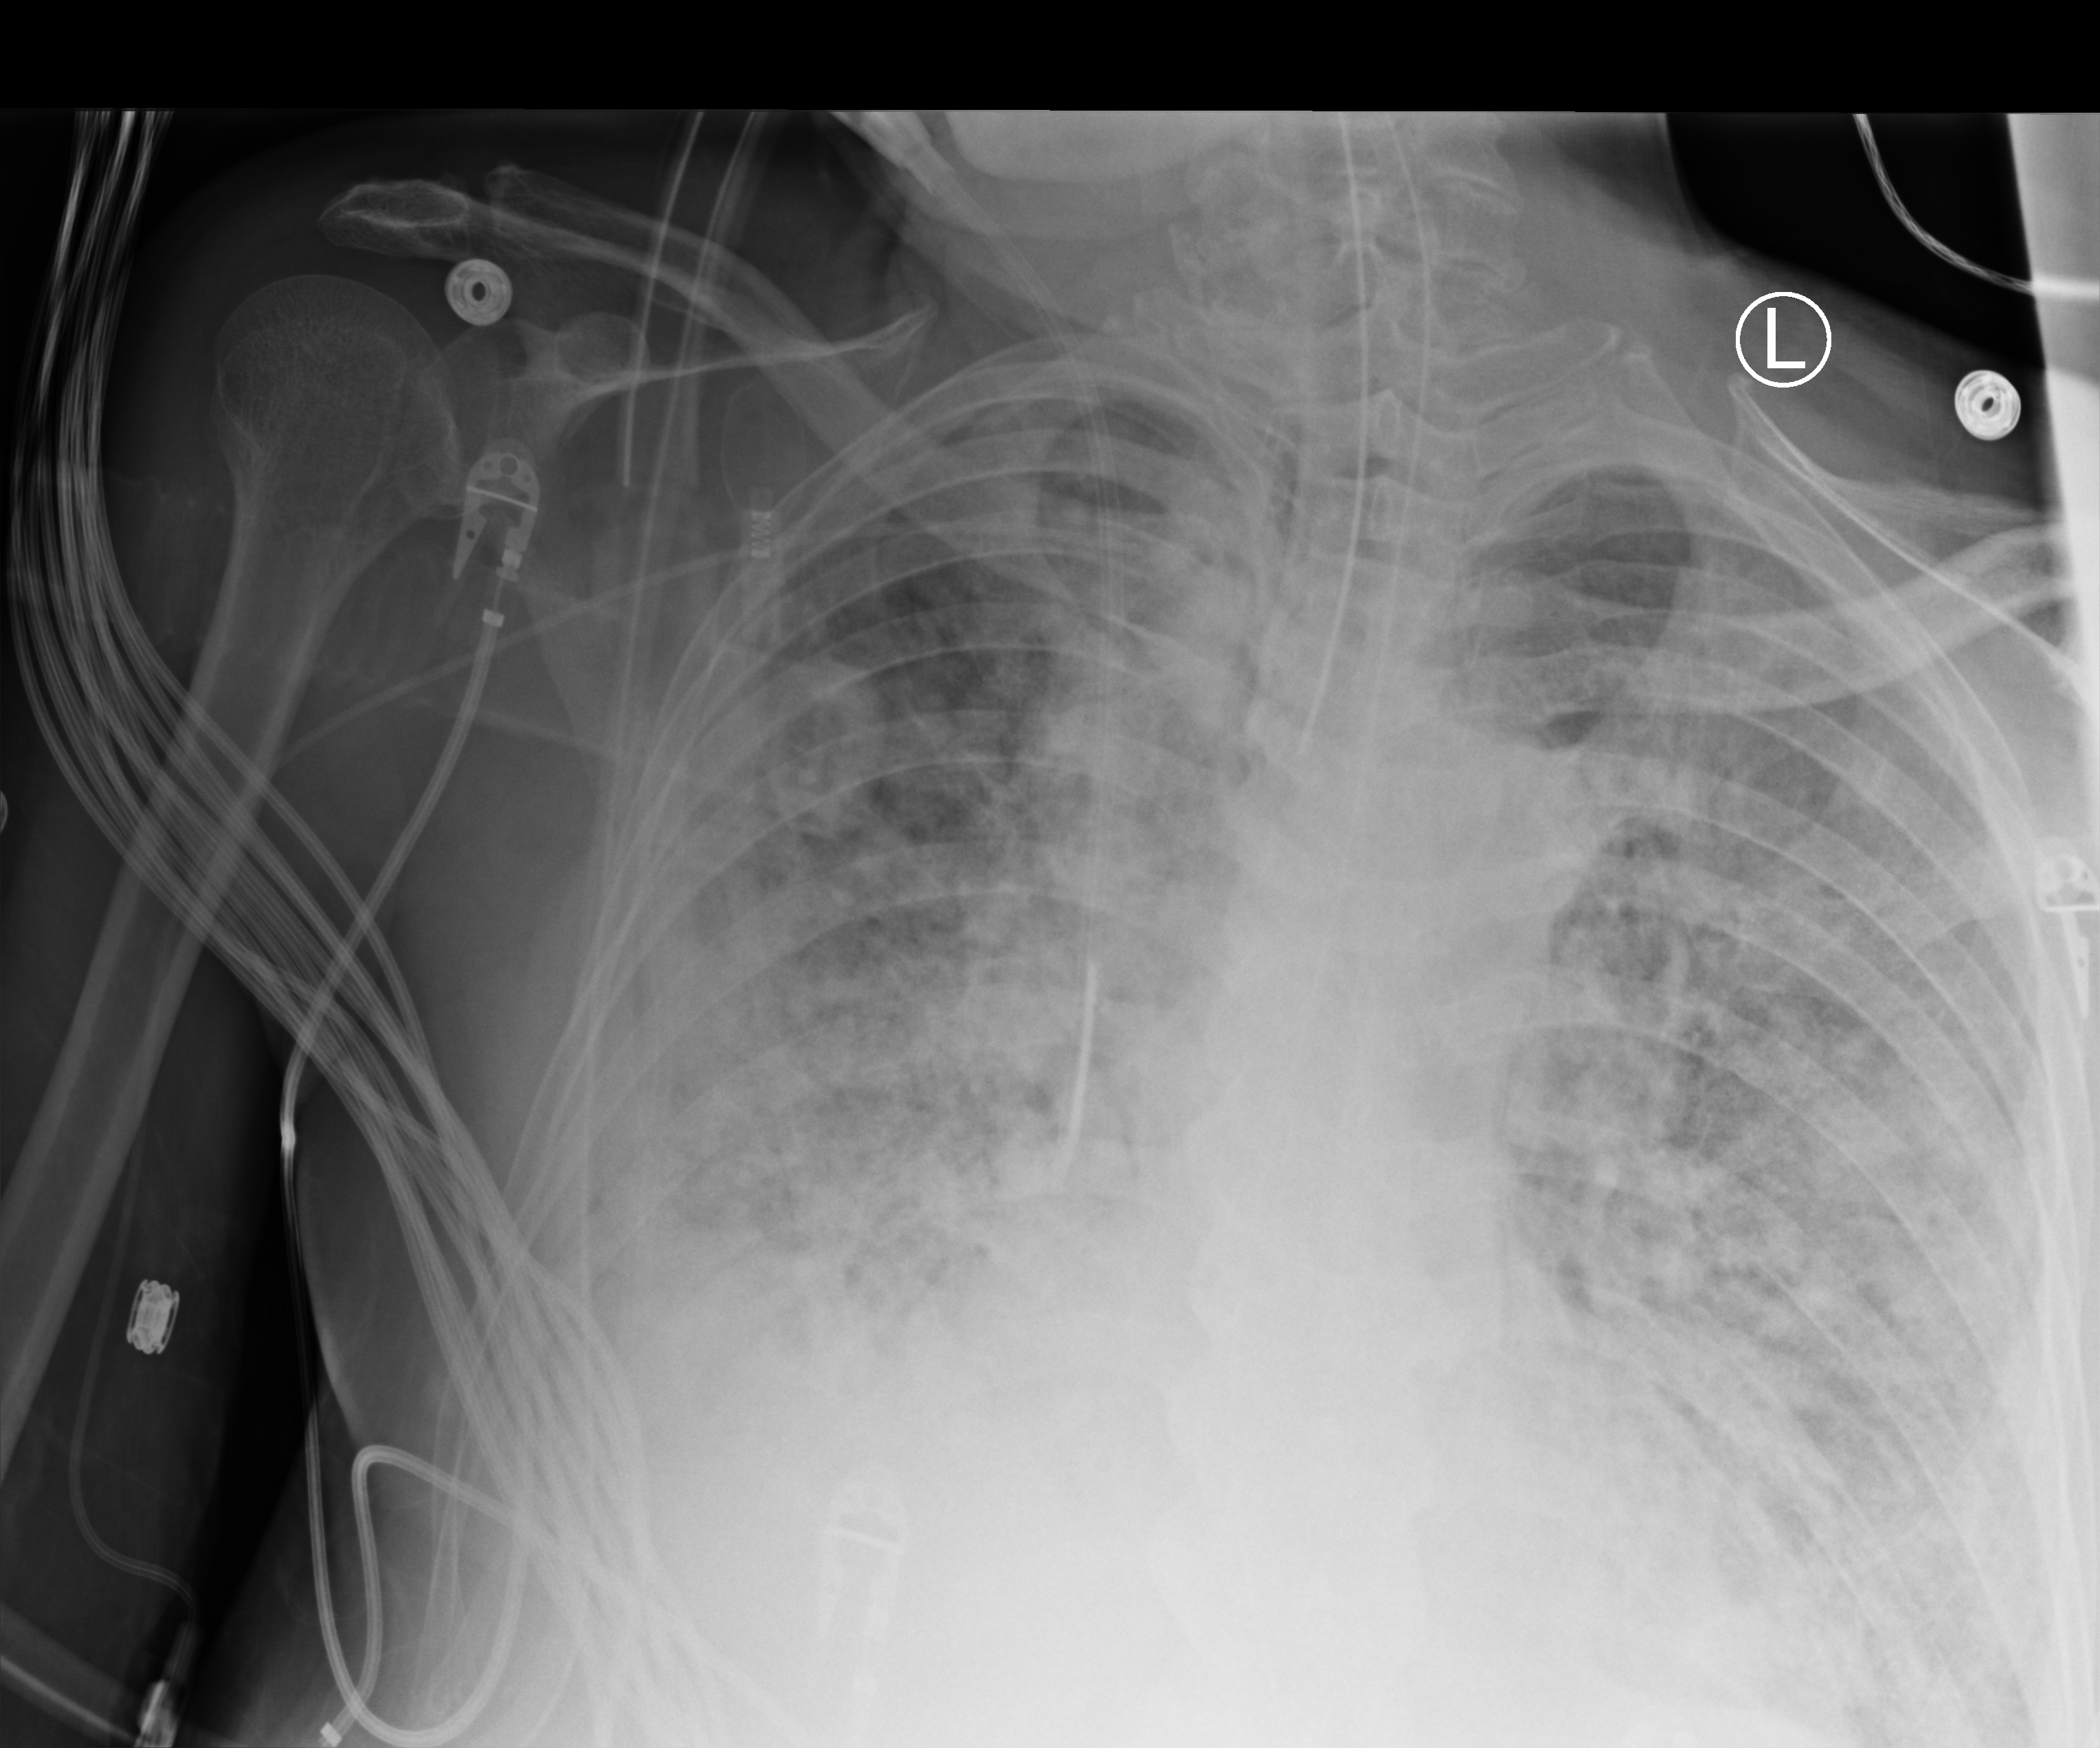
Chest X-ray (portable); anteroposterior (AP) projection. Patient hospitalised with COVID-19; male, aged 60–74 years.
From the hospital-stay record, not from the radiograph (when in the stay this image was taken is not recorded): admitted to intensive care during this hospital stay: yes.